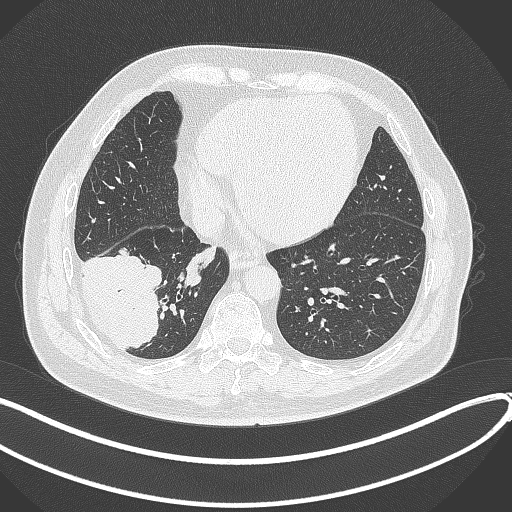
Chest CT, one axial slice; slice 110 of 360 in the series (ordered by position); reconstruction kernel B70f; 120 kVp; lung window (W 1500 / L -600 HU); 1 mm slice thickness; 512 × 512 image matrix. Male patient, age 59 years.
Outlined on this slice (rectangle marked by the reading radiologist):
- lung tumour (recorded histology: adenocarcinoma): bounding box [x1, y1, x2, y2] px = [81, 251, 164, 351]